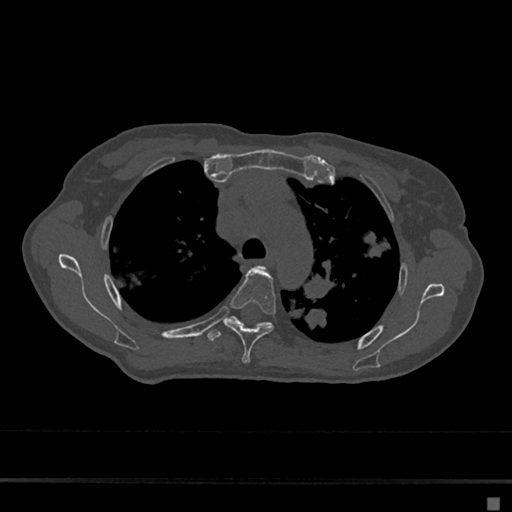
CT including the spine, one axial slice; position 493 of 797 along the scan axis; 120 kVp; bone window (W 1800 / L 400 HU); 0.5 mm slice thickness; 512 × 512 image matrix, field of view 360 × 360 mm. Patient: female, 68 years. From the clinical record (not read from this slice): primary cancer: renal.
Structures marked on this image (semi-automatically segmented with operator editing):
- T4 vertebra: box from (x=224, y=268) to (x=276, y=364) px
- T5 vertebra: (x=207, y=315)–(x=284, y=345)